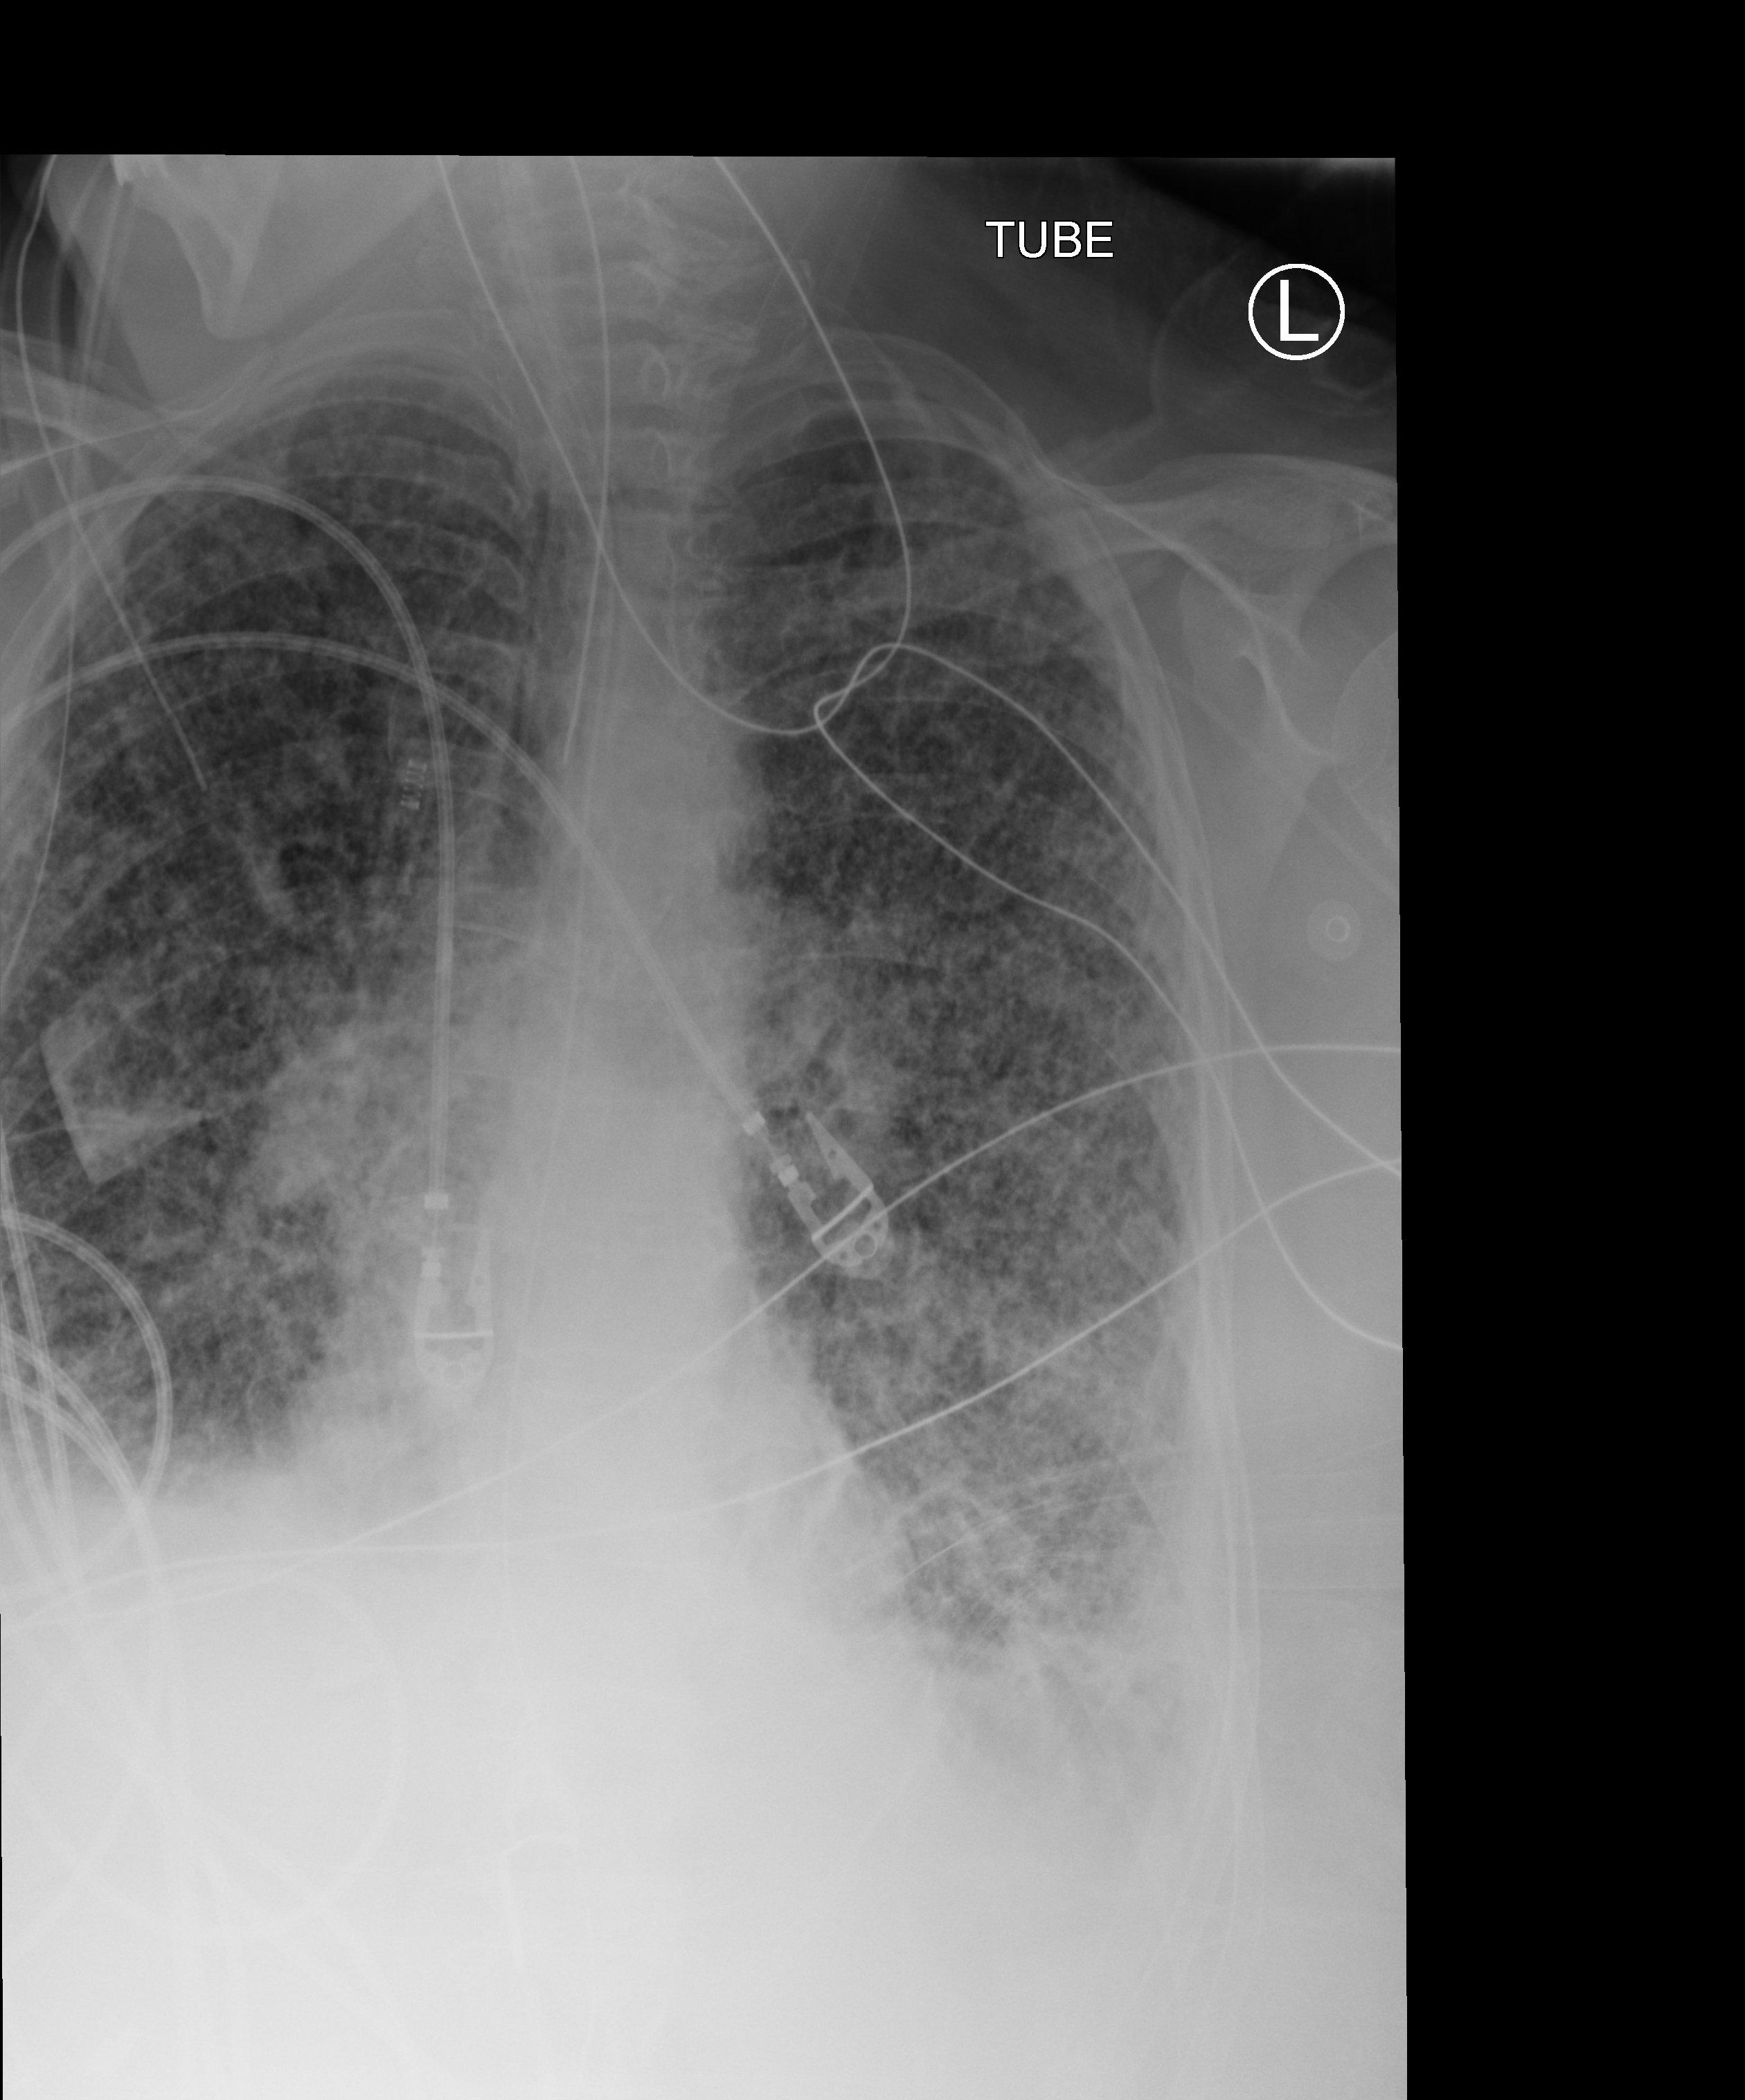
Bedside chest radiograph (computed radiography); anteroposterior (AP) projection. Patient hospitalised with COVID-19; female, aged 60–74 years.
Admission-level facts for this patient (not findings on this image; timing relative to this image not recorded): admitted to intensive care during this hospital stay: yes; hypertension (admission record): no; mechanically ventilated during this hospital stay: yes.